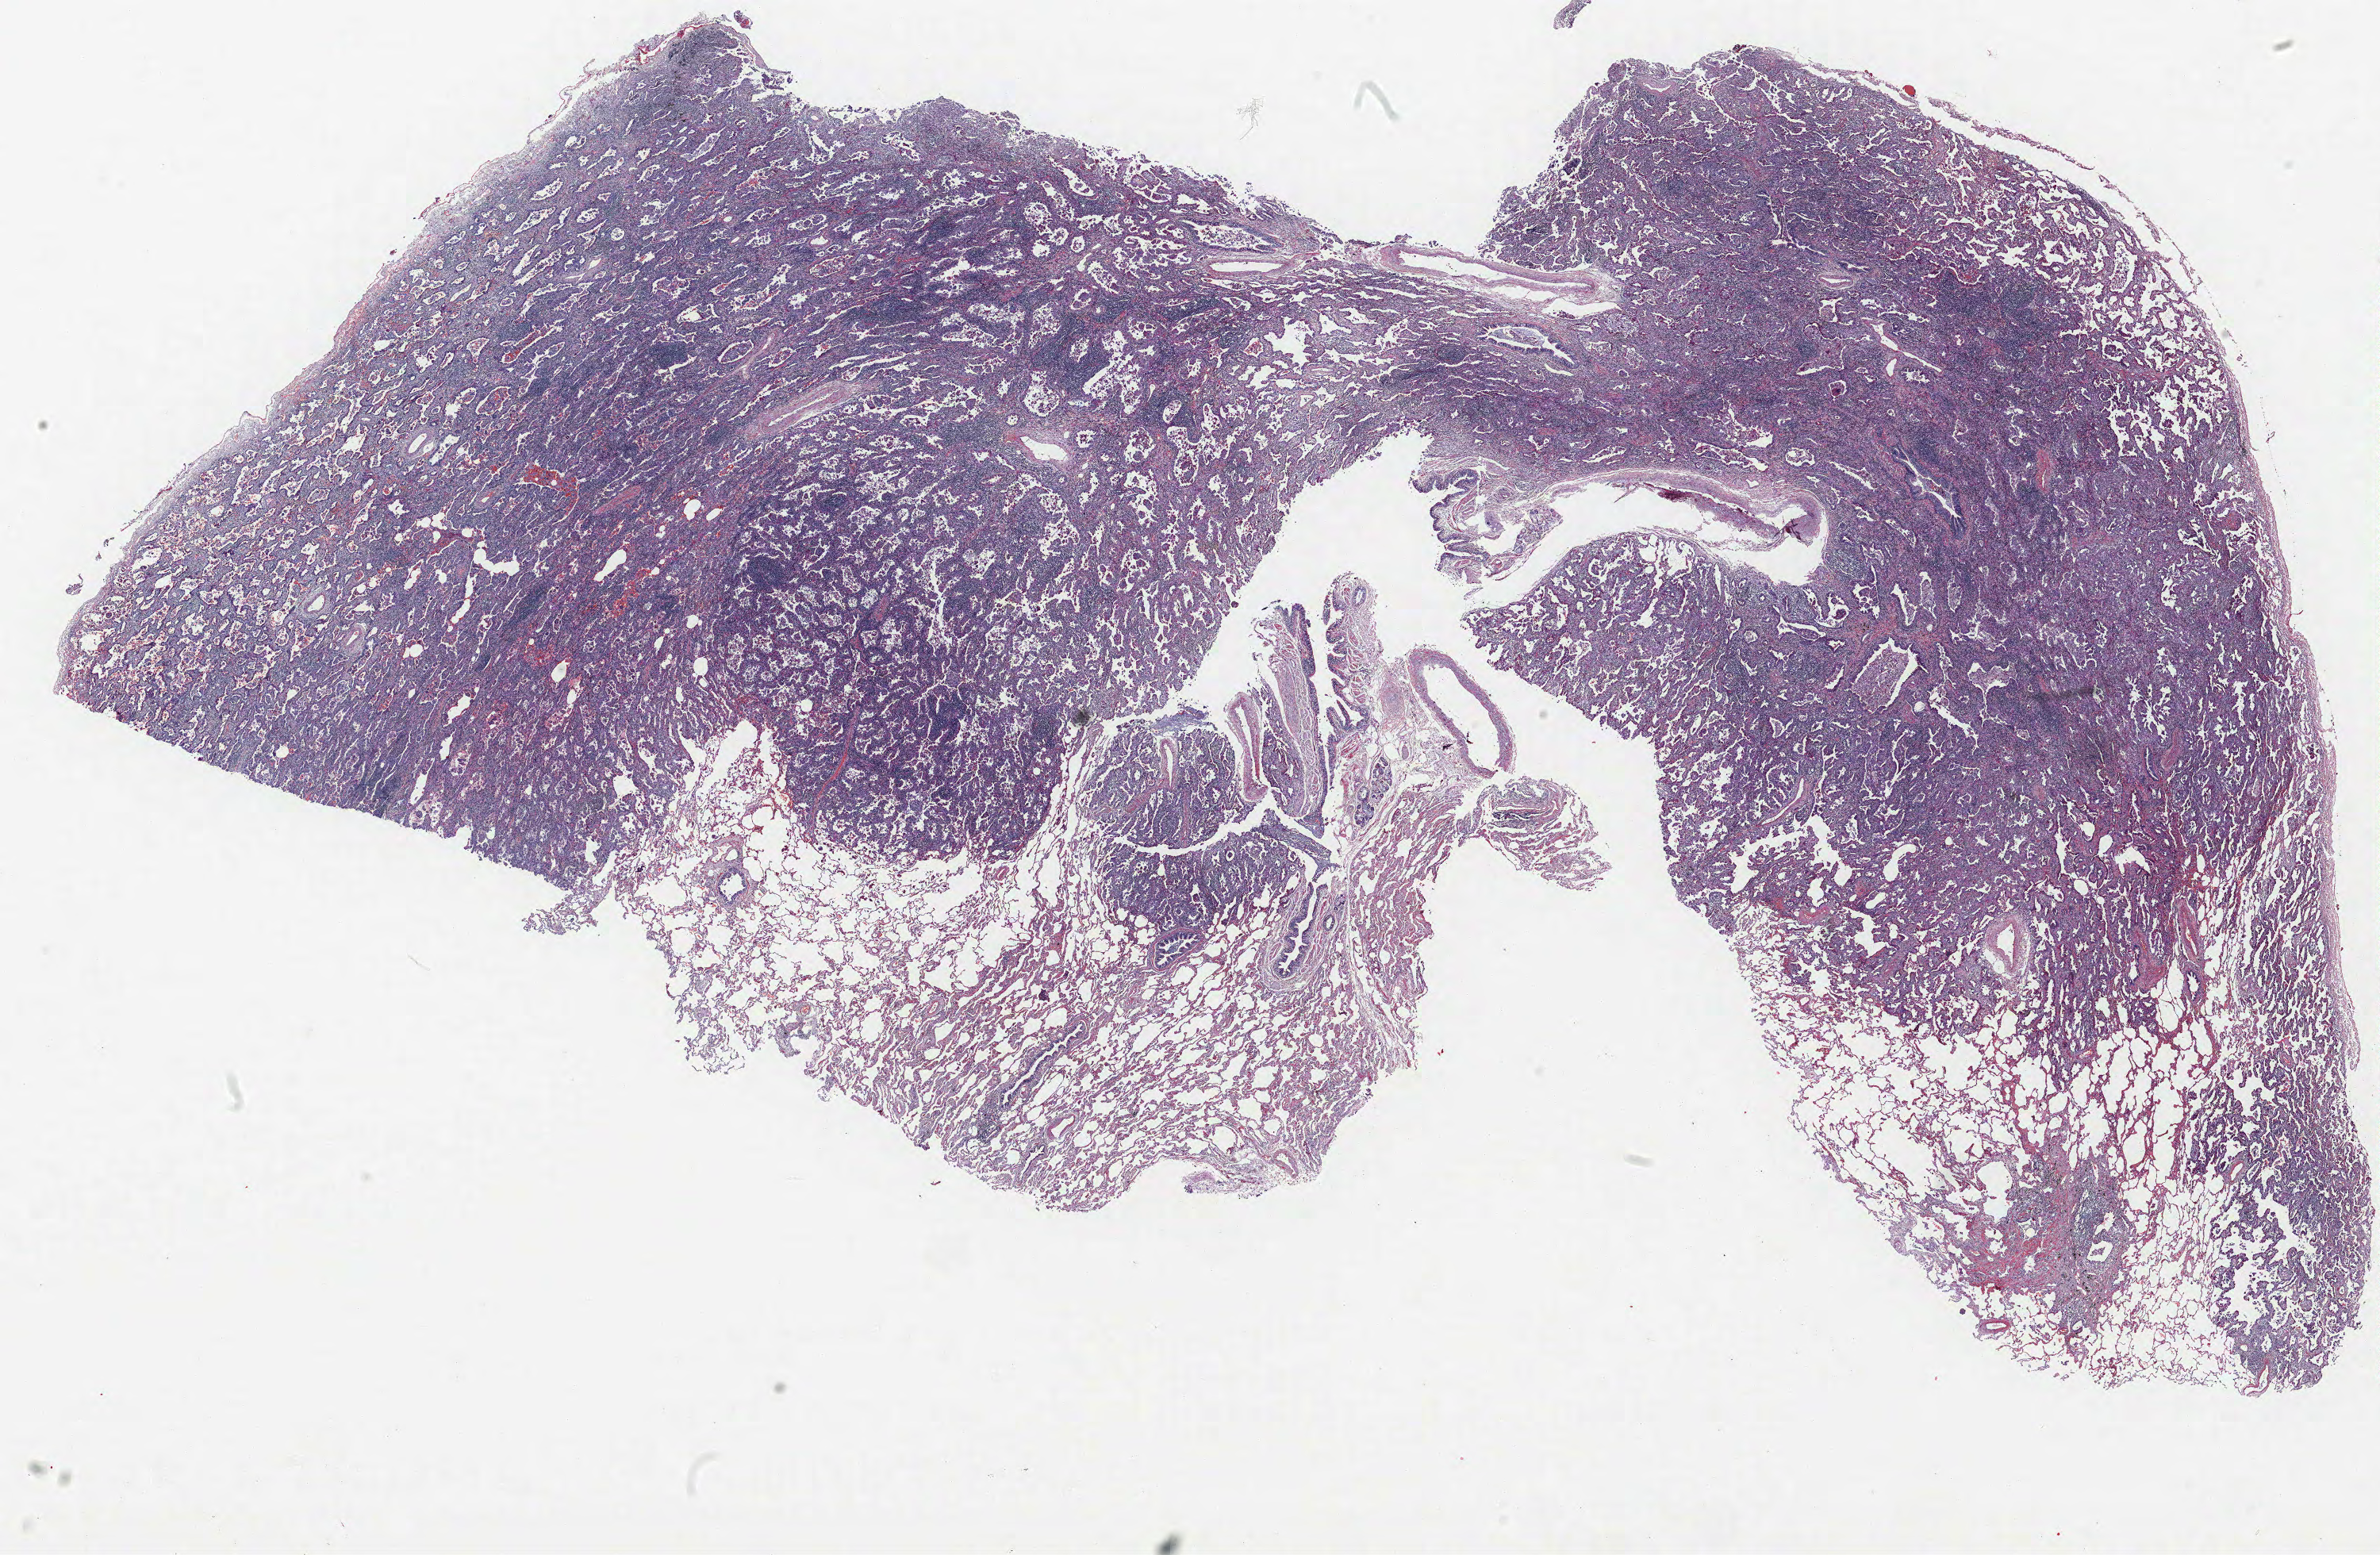
H&E-stained whole-slide image — shown as a low-resolution overview of the whole scanned area (about 24.0 x 15.7 mm, acquisition: 40x scan), formalin-fixed paraffin-embedded (FFPE) section, lung tissue. Female, age 57 at enrolment. Former smoker at enrolment. Grade: well differentiated (G1).
• participant's lung-cancer diagnosis: Adenocarcinoma, NOS
• stage (AJCC 6th edition): IA
• tumour size (pathology): 21 mm
• primary tumour location (clinical record): right middle lobe